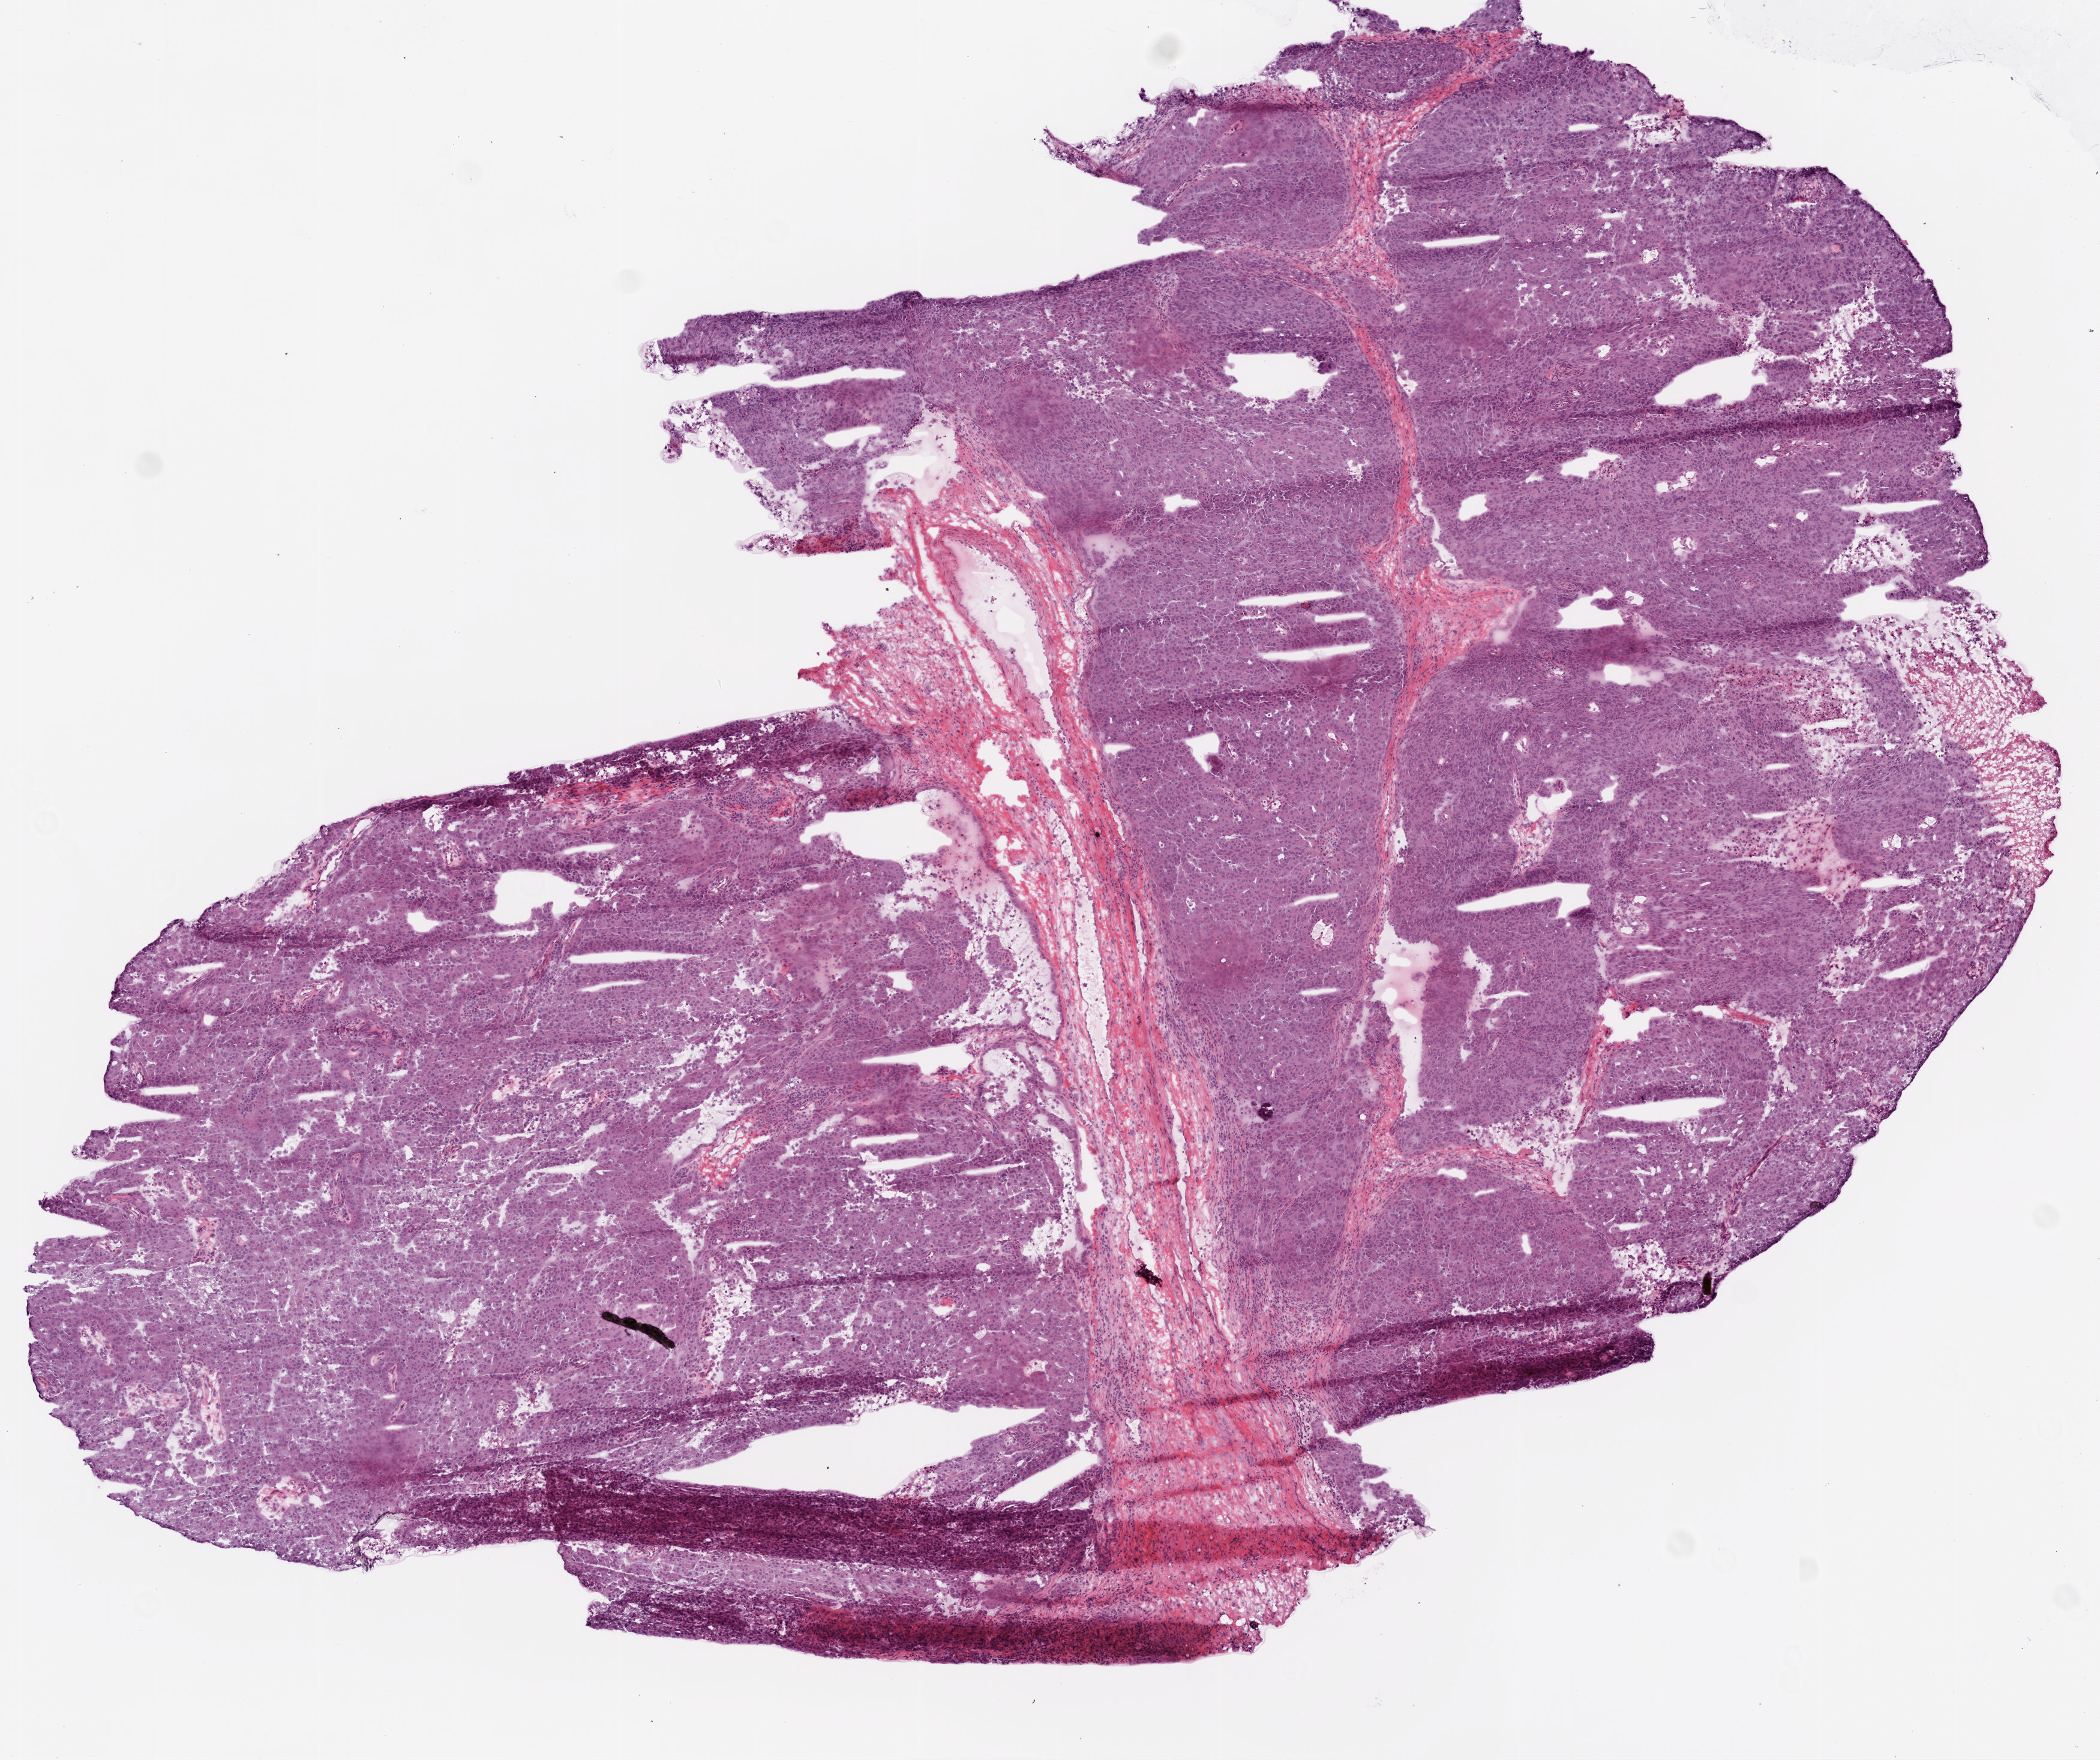
Digitized H&E tissue section (whole slide), shown as a low-resolution overview of the whole scanned area (about 7.0 x 5.9 mm, from a 20x scan); frozen section; primary tumour sample from the ovary. Patient: female, age at initial diagnosis 63 years. Histologic grade: G3 (poorly differentiated). Slide review estimates, as recorded: tumour cells 90%, tumour nuclei 95%, normal cells 0%, stromal cells 8%, necrosis 2%.
- FIGO stage: IV
- pathologic diagnosis: Serous cystadenocarcinoma, NOS